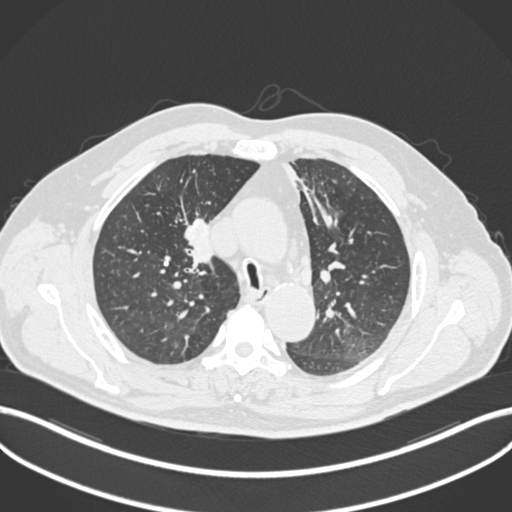
Chest CT, one axial slice; position 138 of 255 along the scan axis; reconstruction kernel B30f; lung window (W 1500 / L -600 HU); 1 mm slice thickness; 512 × 512 image matrix, field of view 400 × 400 mm. Patient: male, 60 years. Case-level facts recorded for this patient, not image findings: clinical TNM (as recorded): T1b N1 M0.
Annotated regions visible in this slice (rectangle marked by the reading radiologist):
- lung tumour (recorded histology: squamous cell carcinoma): box from (x=174, y=211) to (x=225, y=281) px